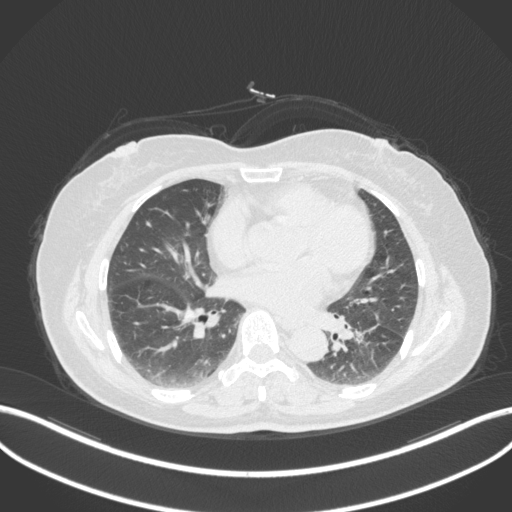
Chest CT, one axial slice. Position 169 of 307 along the scan axis. 120 kVp. Lung window (W 1500 / L -600 HU). 1 mm slice thickness. 512 × 512 image matrix, field of view 400 × 400 mm. Patient: female, 59 years. From the clinical record (not read from this slice): clinical TNM (as recorded): T2a N0 M0.
Annotated regions visible in this slice (bounding box drawn by a radiologist):
- lung tumour (recorded histology: adenocarcinoma): bounding box <354,308,385,350> (left, top, right, bottom; pixels)